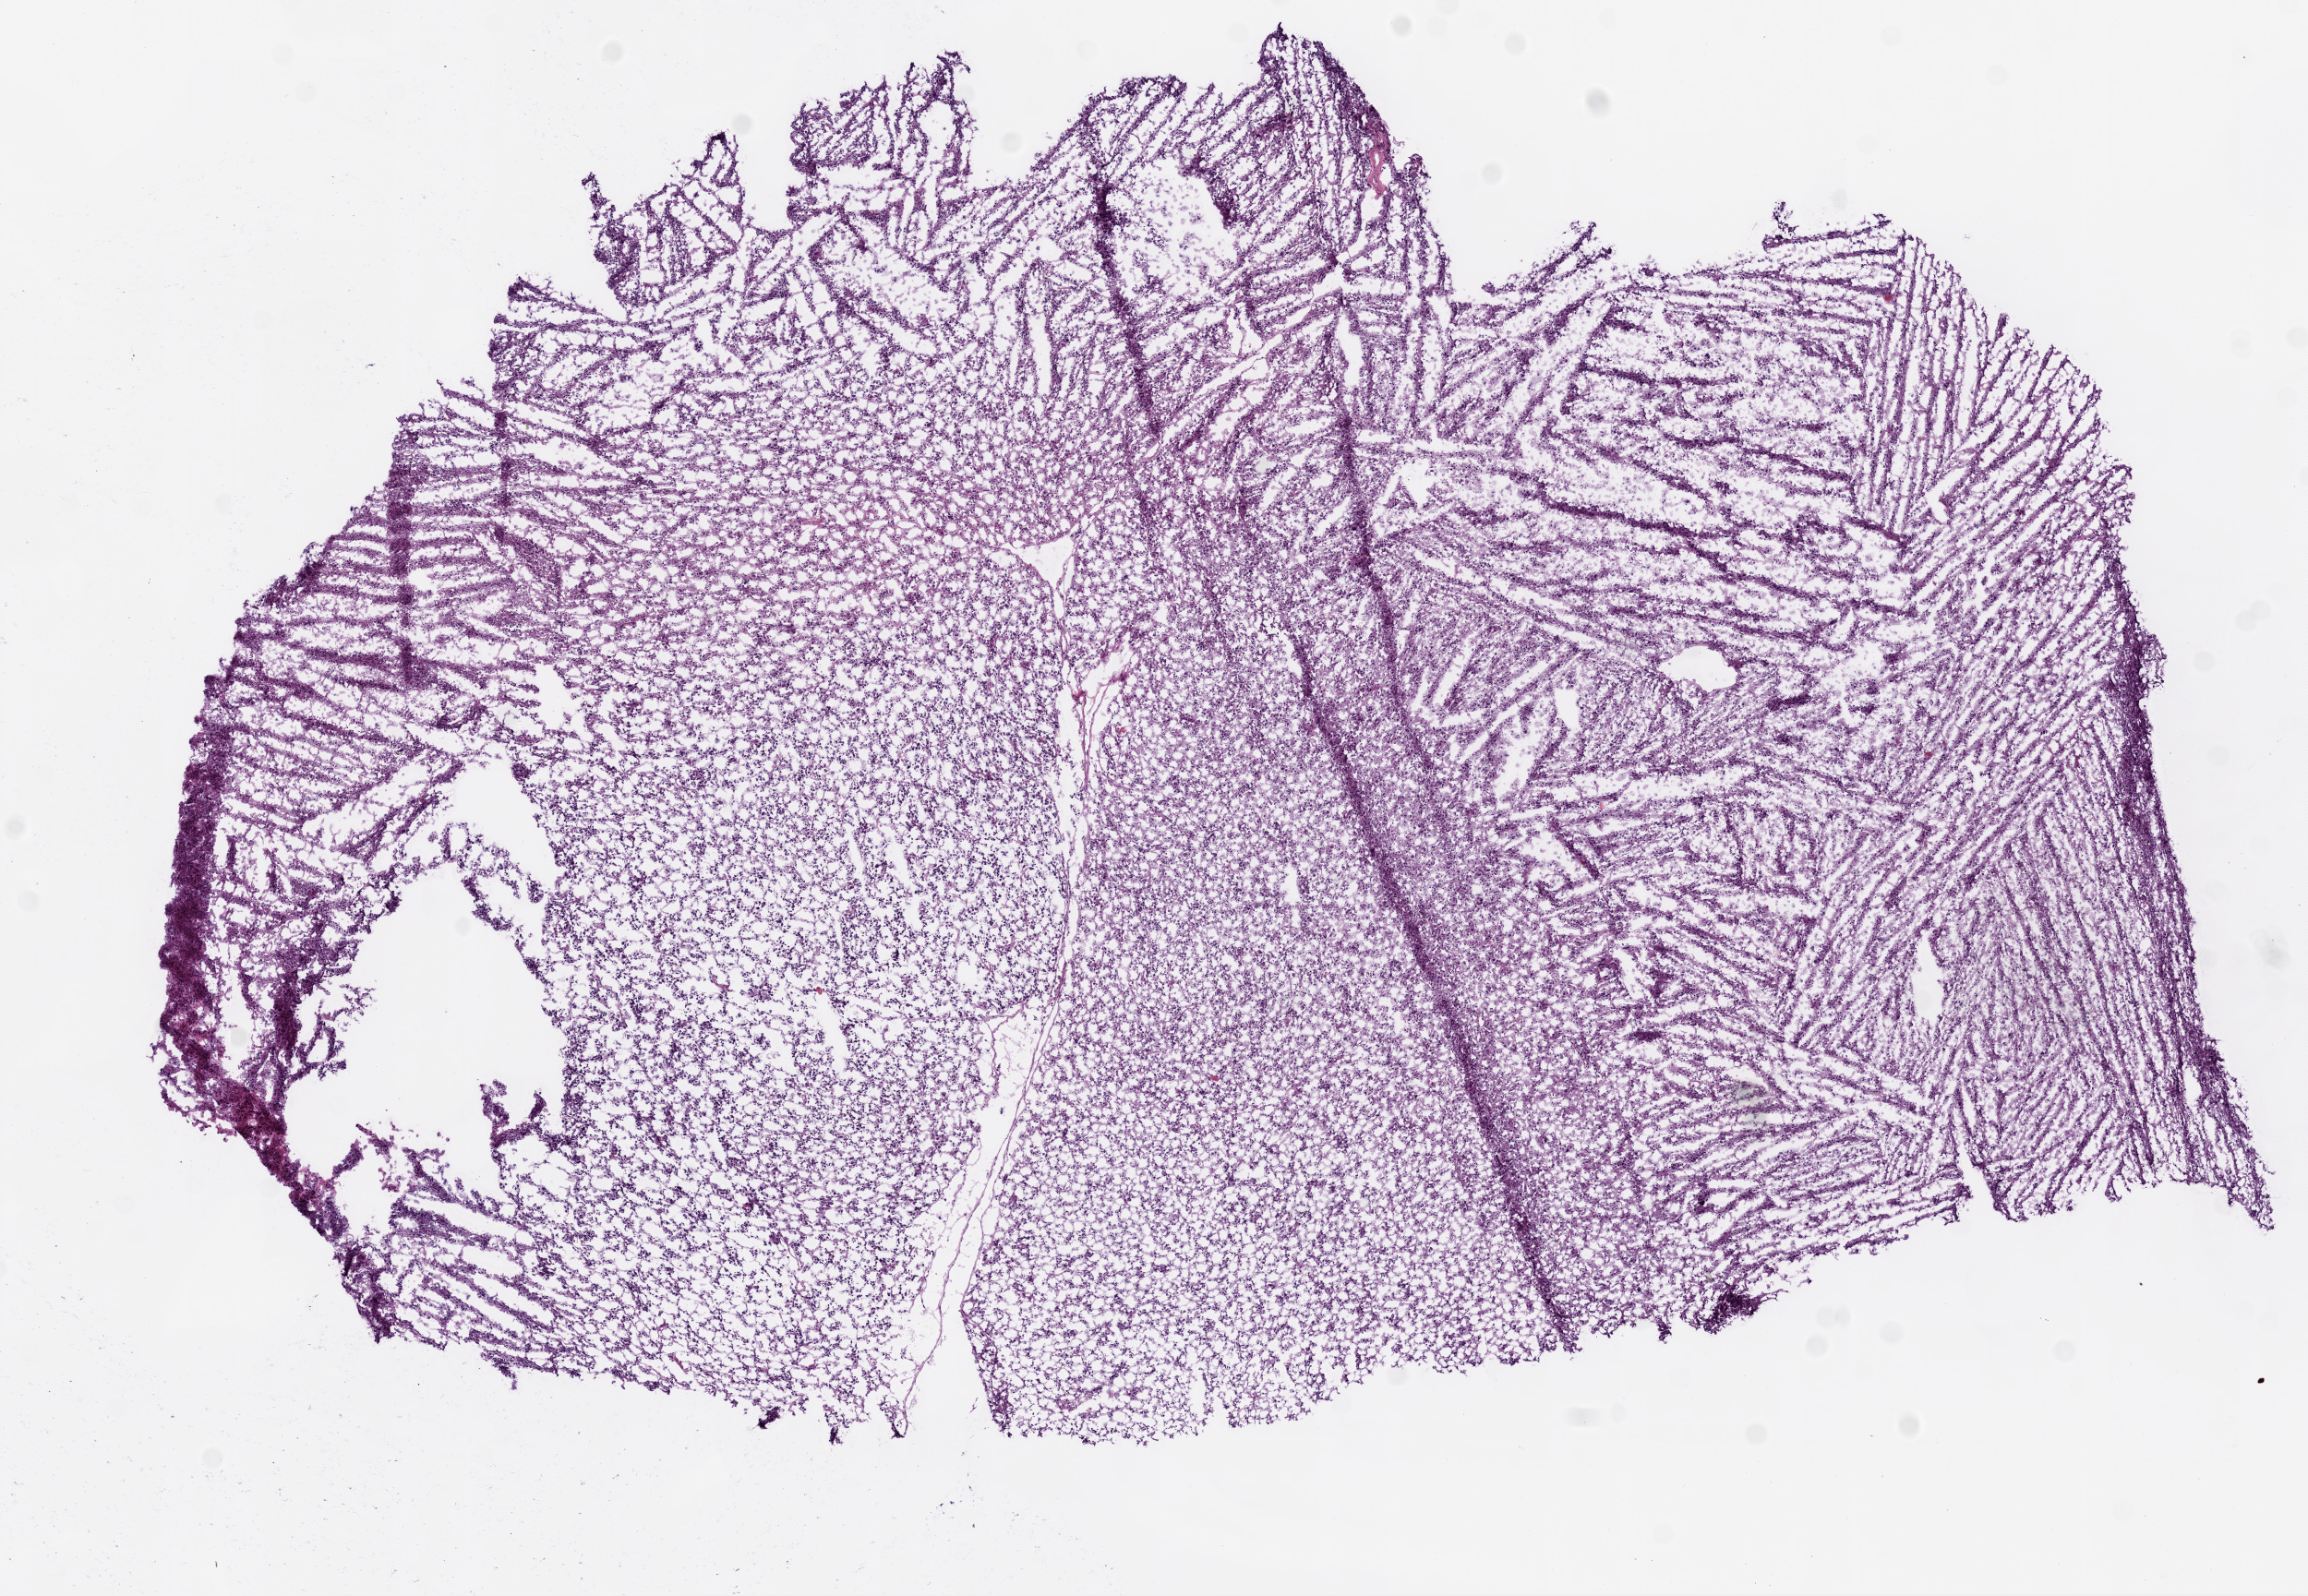
Hematoxylin and eosin (H&E) stained whole-slide image — a low-resolution overview of the entire scanned area, about 10.0 x 6.9 mm, frozen section, brain, primary tumour sample. Male patient; age at initial diagnosis 51 years. Slide review estimates, as recorded: tumour cells 98%, tumour nuclei 85%, normal cells 0%, stromal cells 0%, necrosis 2%.
Diagnosis: Glioblastoma.